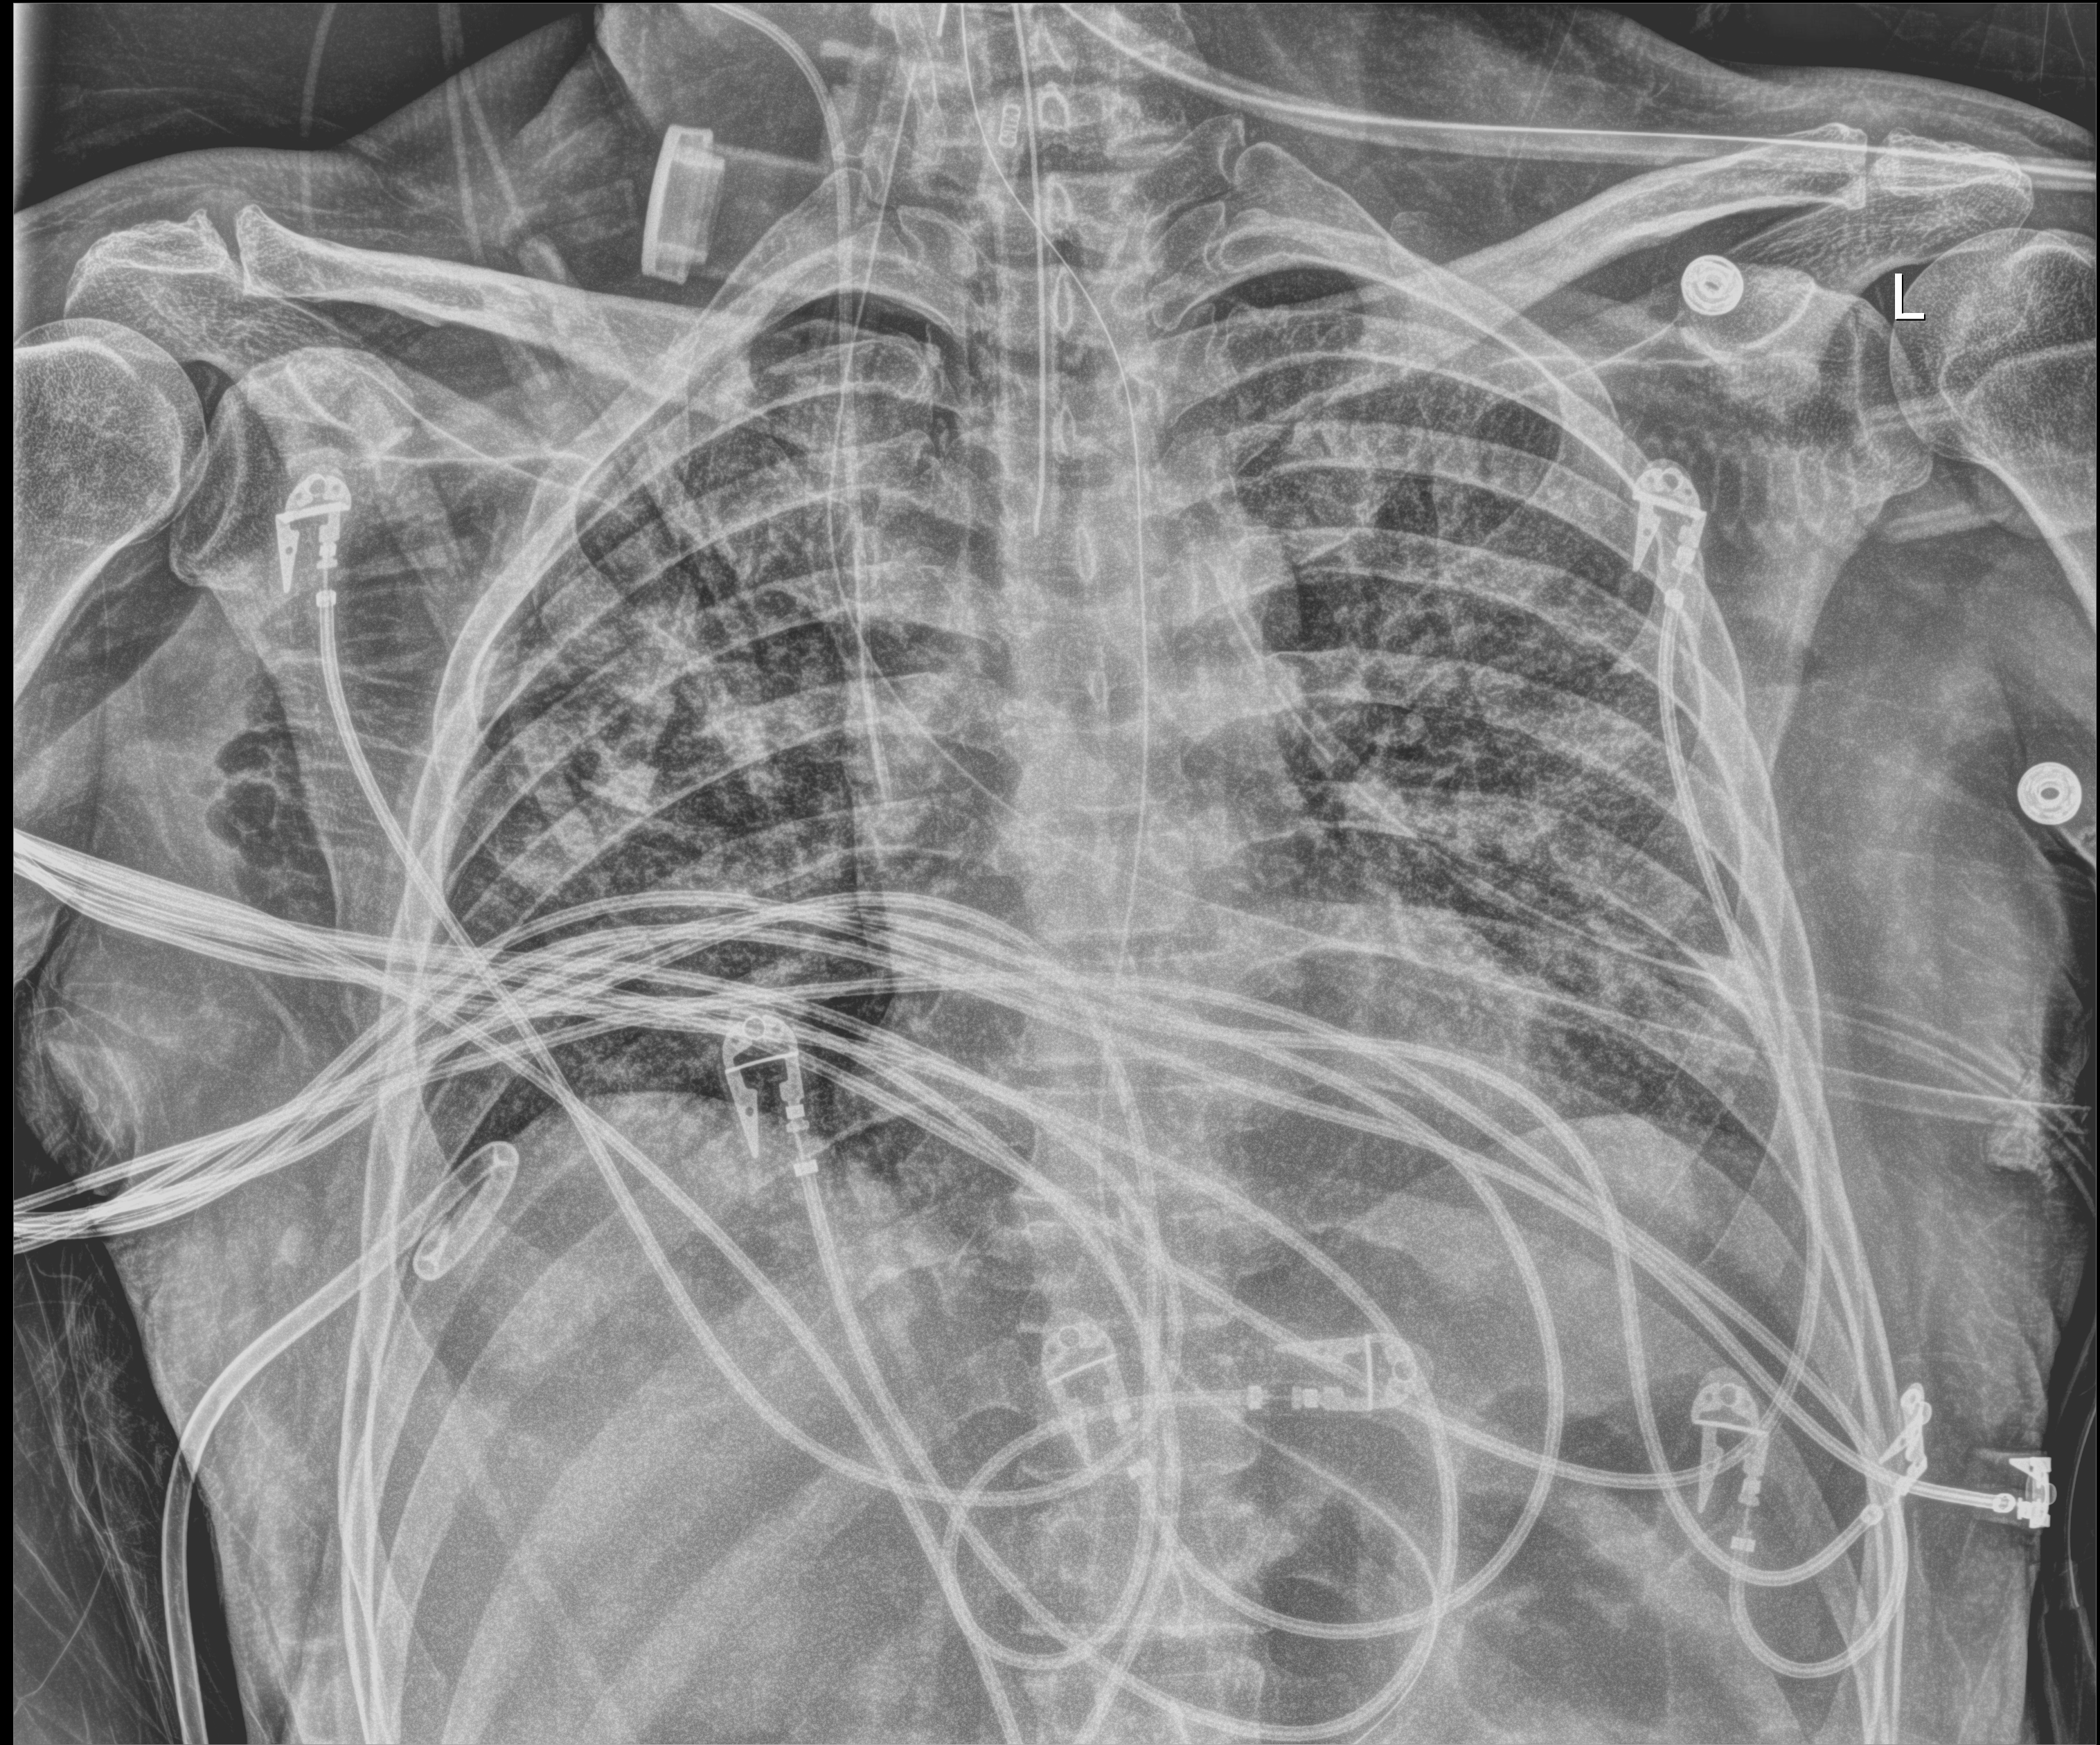
Portable chest radiograph; anteroposterior (AP) projection. Patient hospitalised with COVID-19; male, aged 18–59 years.
Hospital-stay facts (about this admission, not read from this image; timing relative to this image not recorded):
- hypertension (admission record): no
- admitted to intensive care during this hospital stay: yes